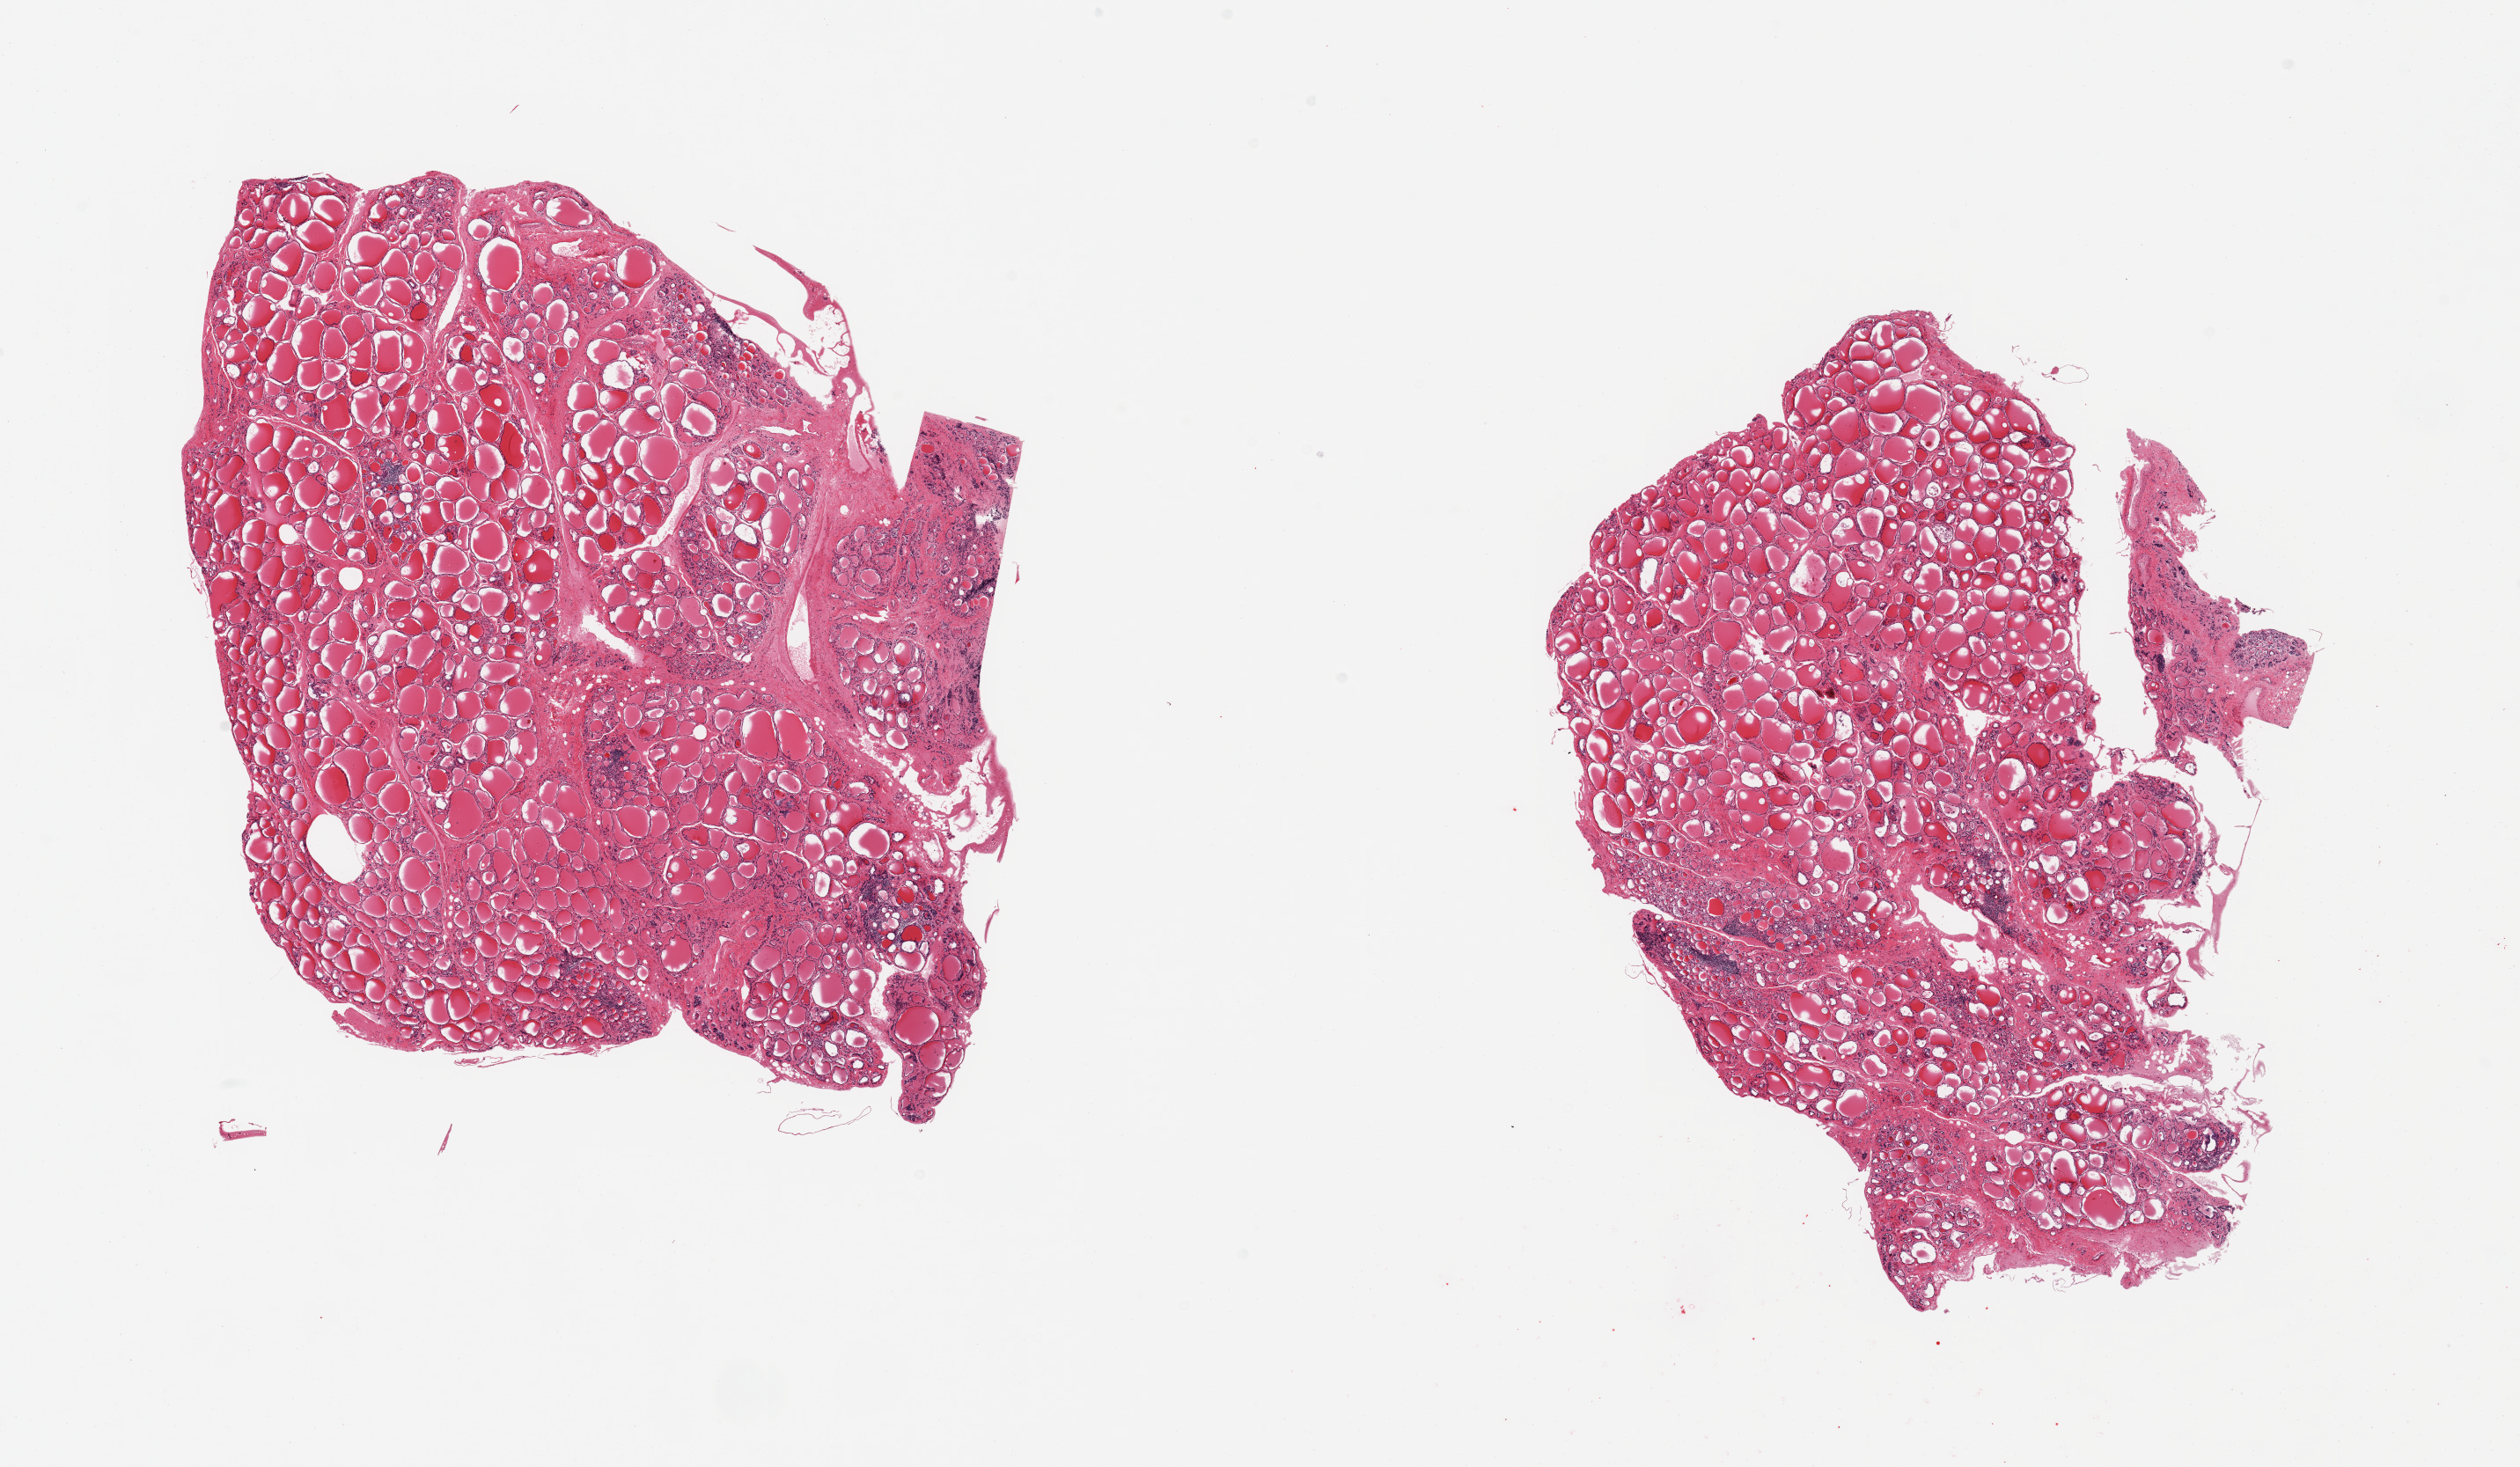
Whole-slide image, hematoxylin and eosin (H&E) stain, brightfield, shown as a low-resolution overview of the whole scanned area (about 22.6 x 13.2 mm); PAXgene-fixed, paraffin-embedded tissue; target tissue: thyroid; donor tissue sample.
Reviewer comment on this tissue sample: 2 pieces, fibrosis/regressive changes.